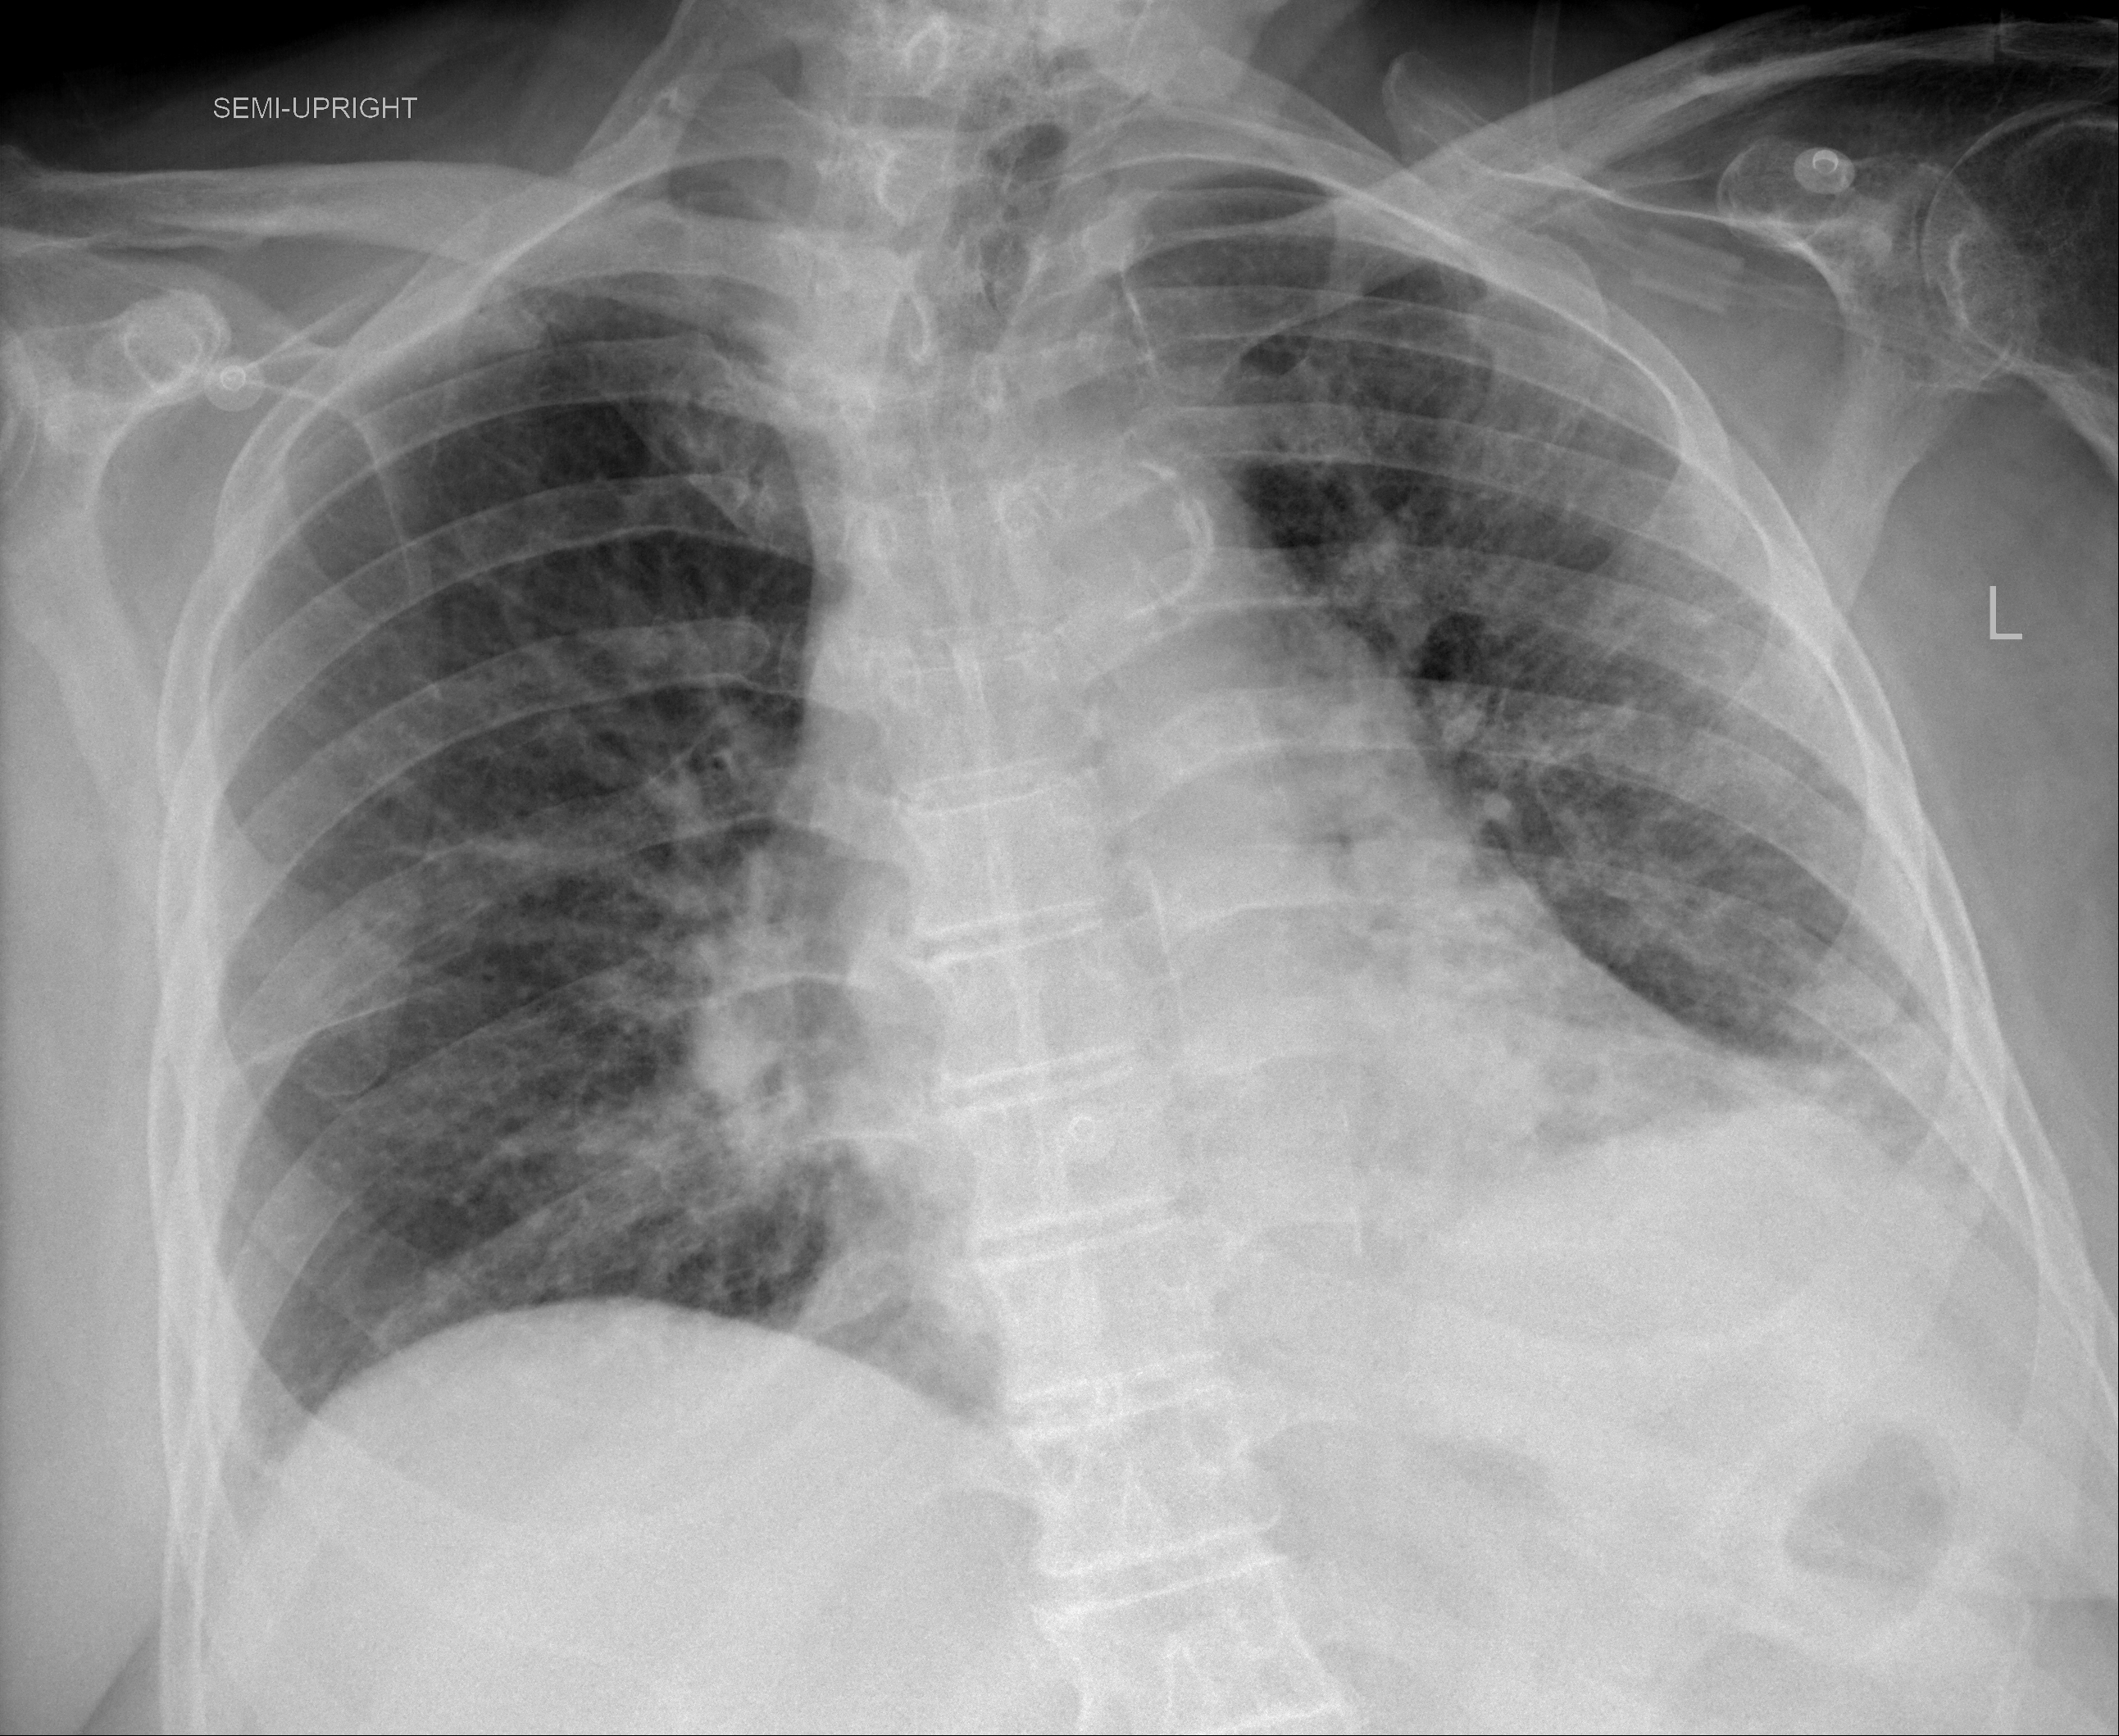
Portable chest radiograph, AP projection. Male patient, age 89 years; imaged 4 days after the COVID-19 diagnosis.
Radiologist key findings (as recorded): The opacities within the right mid lung and base persist but have improved from the prior examination.